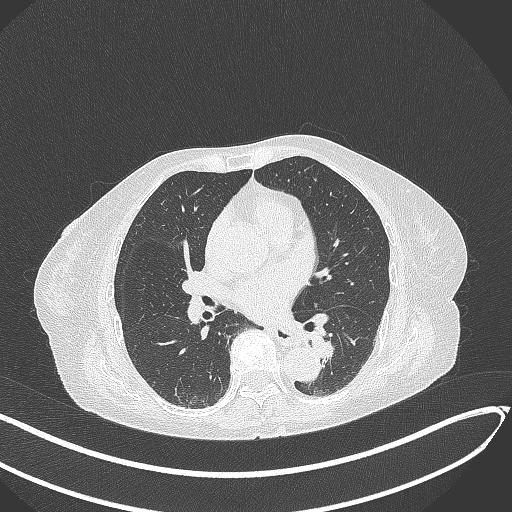
Chest CT, one axial slice. Slice 125 of 324 in the series (ordered by position). Reconstruction kernel B70f. 120 kVp. Lung window (W 1500 / L -600 HU). 512 × 512 image matrix, field of view 400 × 400 mm. Patient: female, 82 years. Case-level facts recorded for this patient, not image findings: clinical TNM (as recorded): T1b N0 M1.
Annotated regions visible in this slice (rectangle marked by the reading radiologist):
- lung tumour (recorded histology: adenocarcinoma): bounding box <308,332,340,363> (left, top, right, bottom; pixels)